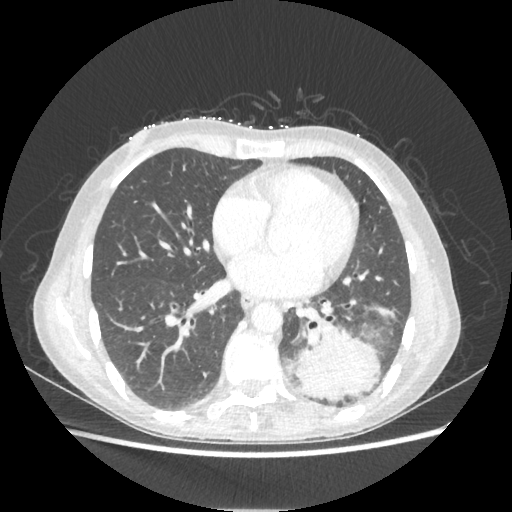
Chest CT, one axial slice. Position 95 of 221 along the scan axis. Reconstruction kernel STANDARD. 80 kVp. Lung window (W 1500 / L -600 HU). 1.25 mm slice thickness. 512 × 512 image matrix, field of view 360 × 360 mm. Female patient, age 53 years. Case-level facts recorded for this patient, not image findings: clinical TNM (as recorded): T3 N0 M0.
Structures marked on this image (rectangle marked by the reading radiologist):
- lung tumour (recorded histology: adenocarcinoma): bounding box <290,321,382,398> (left, top, right, bottom; pixels)